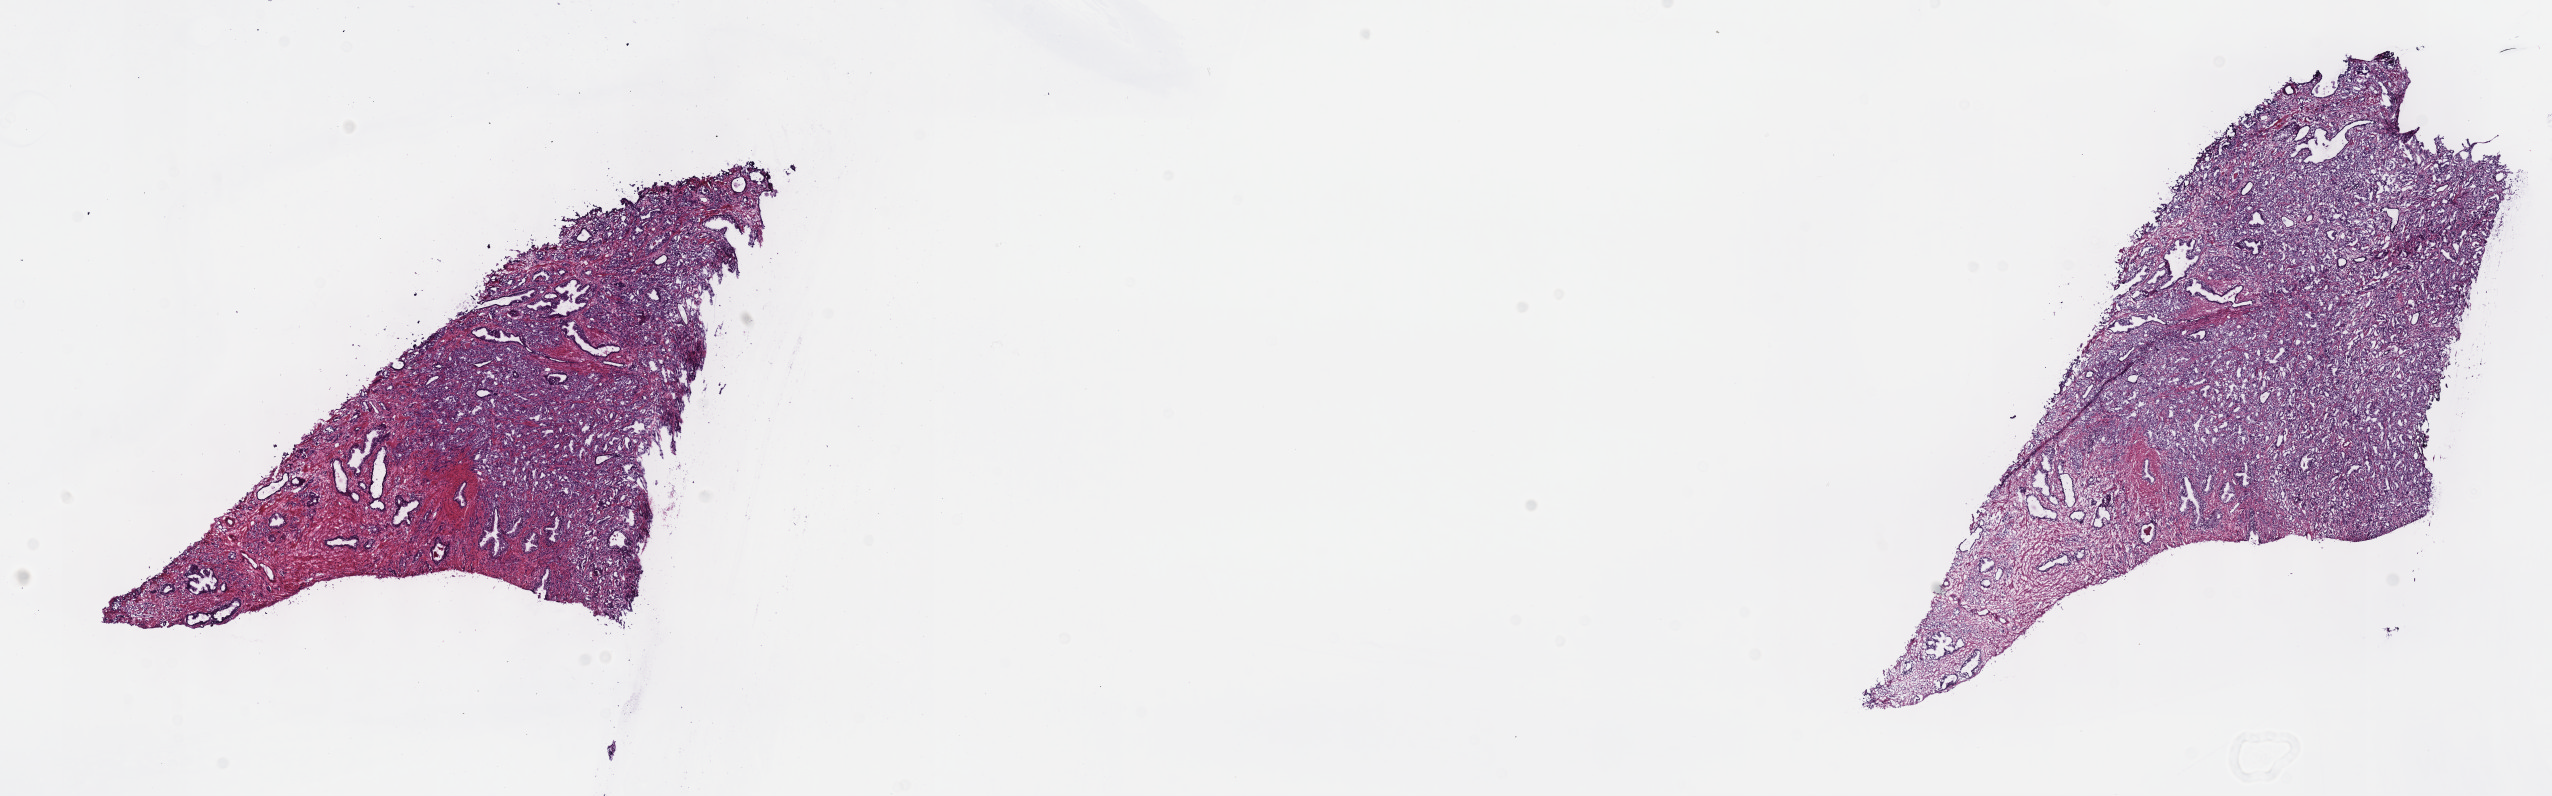
Whole-slide histology image, H&E — low-resolution overview of the scanned area, about 20.6 x 6.4 mm (from a 40x scan); frozen section; sample: primary tumour, prostate. Patient: male, age at initial diagnosis 53 years. Gleason score: 7 (3+4). Composition of this section per pathologist review: tumour cells 60%, tumour nuclei 70%, normal cells 30%, stromal cells 10%, necrosis 0%. Infiltration values recorded for this section: lymphocyte infiltration 0%, monocyte infiltration 0%, neutrophil infiltration 0%.
* diagnosis: Adenocarcinoma, NOS